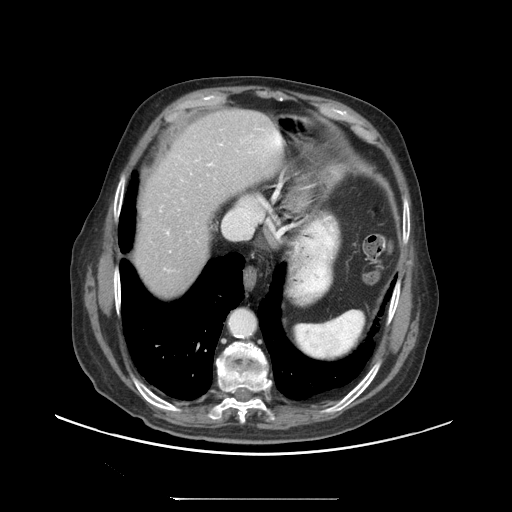
Contrast-enhanced abdominal CT (liver protocol), one axial slice. Slice 83 of 97 in the series (ordered by position). Reconstruction kernel STANDARD. Soft-tissue window (W 400 / L 40 HU). 2.5 mm slice thickness. 512 × 512 image matrix, field of view 450 × 450 mm. Case-level facts recorded for this patient, not image findings: diagnosis: hepatocellular carcinoma (patient treated with transarterial chemoembolisation; whether this scan precedes or follows treatment is not stated here); TNM stage (as recorded): Stage-IIIC; Child-Pugh class: A; tumour differentiation: well differentiated; tumour nodularity: uninodular.
Outlined on this slice (semi-automatically segmented with operator editing):
- abdominal aorta: bounding box <231,309,256,336> (left, top, right, bottom; pixels)
- liver parenchyma outside the tumour (the mass and vessels are separate outlines, so this box may not span the whole liver): <134,110,282,296>
- liver vessels: <167,131,281,234>